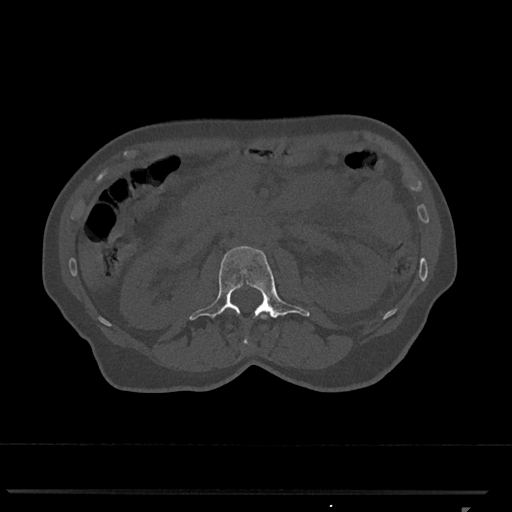
CT including the spine, one axial slice; position 349 of 793 along the scan axis; 120 kVp; bone window (W 1800 / L 400 HU); 0.5 mm slice thickness; 512 × 512 image matrix. Female patient, age 62 years. Case-level facts recorded for this patient, not image findings: primary cancer: renal.
Outlined on this slice (semi-automatically segmented with operator editing):
- L1 vertebra: box from (x=243, y=314) to (x=268, y=345) px
- L2 vertebra: (x=189, y=246)–(x=310, y=320)